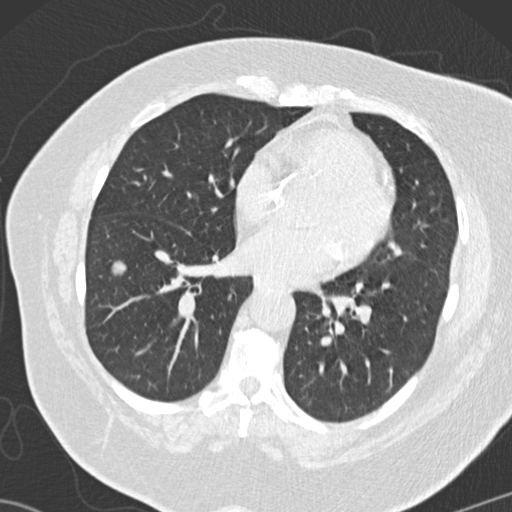
Low-dose screening chest CT, one axial slice; slice 60 of 146 in the series (ordered by position); reconstruction kernel B30f; 120 kVp; lung window (W 1500 / L -600 HU); 2 mm slice thickness; 512 × 512 image matrix.
Structures marked on this image (expert manual segmentation):
- lesion 2 (tumor, lower lobe of right lung): box from (x=110, y=259) to (x=129, y=278) px